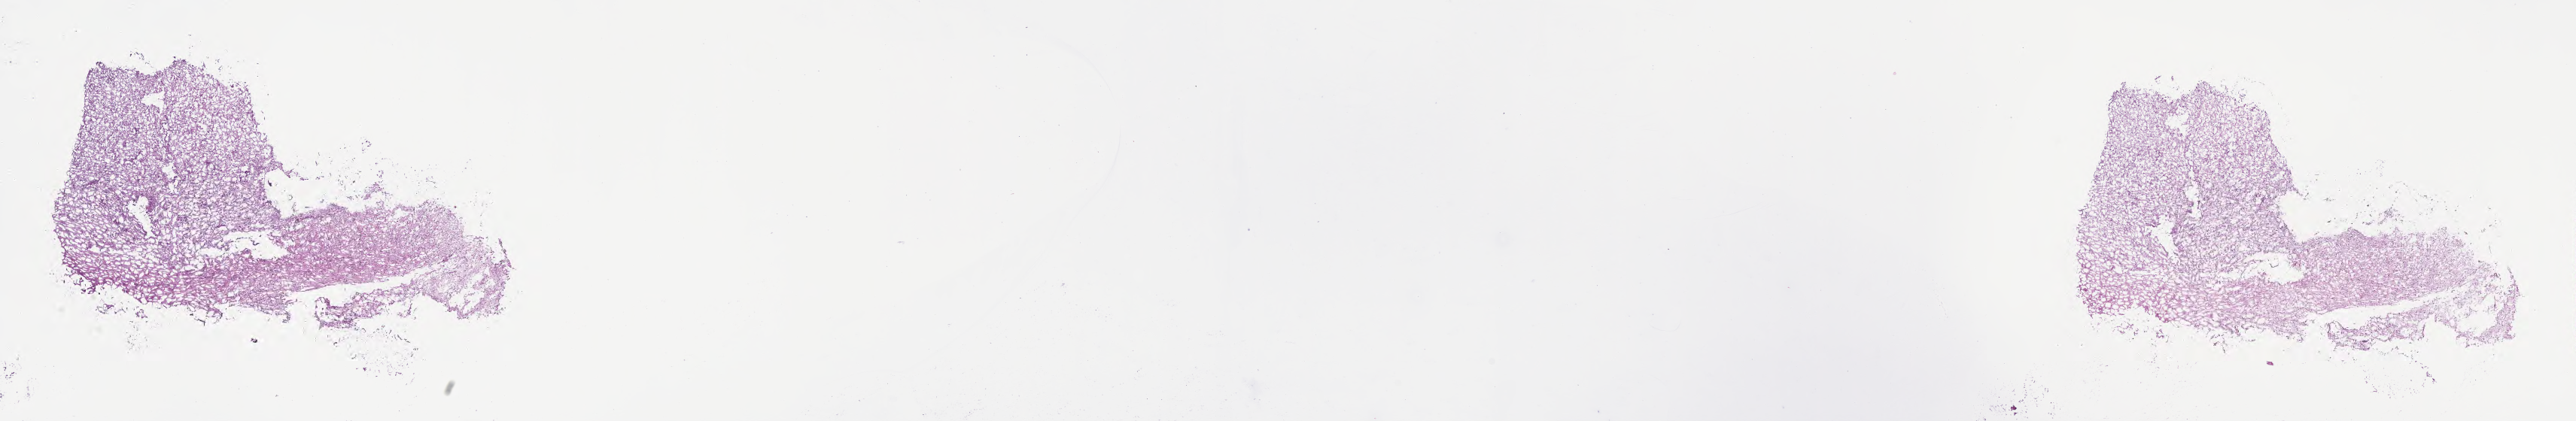
Haematoxylin and eosin whole-slide image of tumor tissue from the brain — low-resolution overview of the scanned area, about 27.7 x 4.5 mm, frozen section. Patient male; age 36 months (3 years).
• diagnosis (ICD-O-3 morphology term): Pilocytic astrocytoma